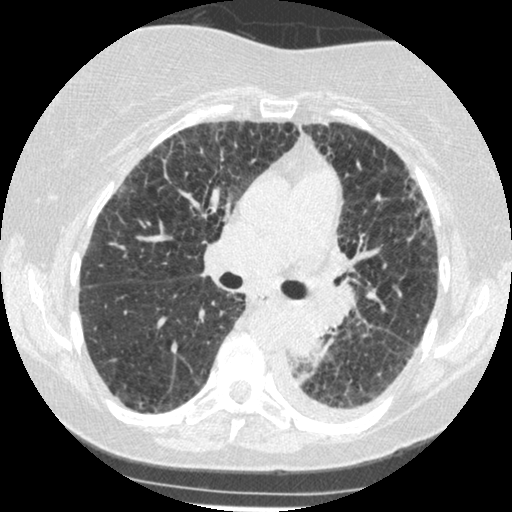
Low-dose screening chest CT, one axial slice; slice 155 of 341 in the series (ordered by position); reconstruction kernel STANDARD; lung window (W 1500 / L -600 HU); 1.25 mm slice thickness; 512 × 512 image matrix.
Annotated regions visible in this slice (manually delineated by an expert):
- lesion 1 (tumor, lower lobe of left lung): bounding box <288,307,329,360> (left, top, right, bottom; pixels)